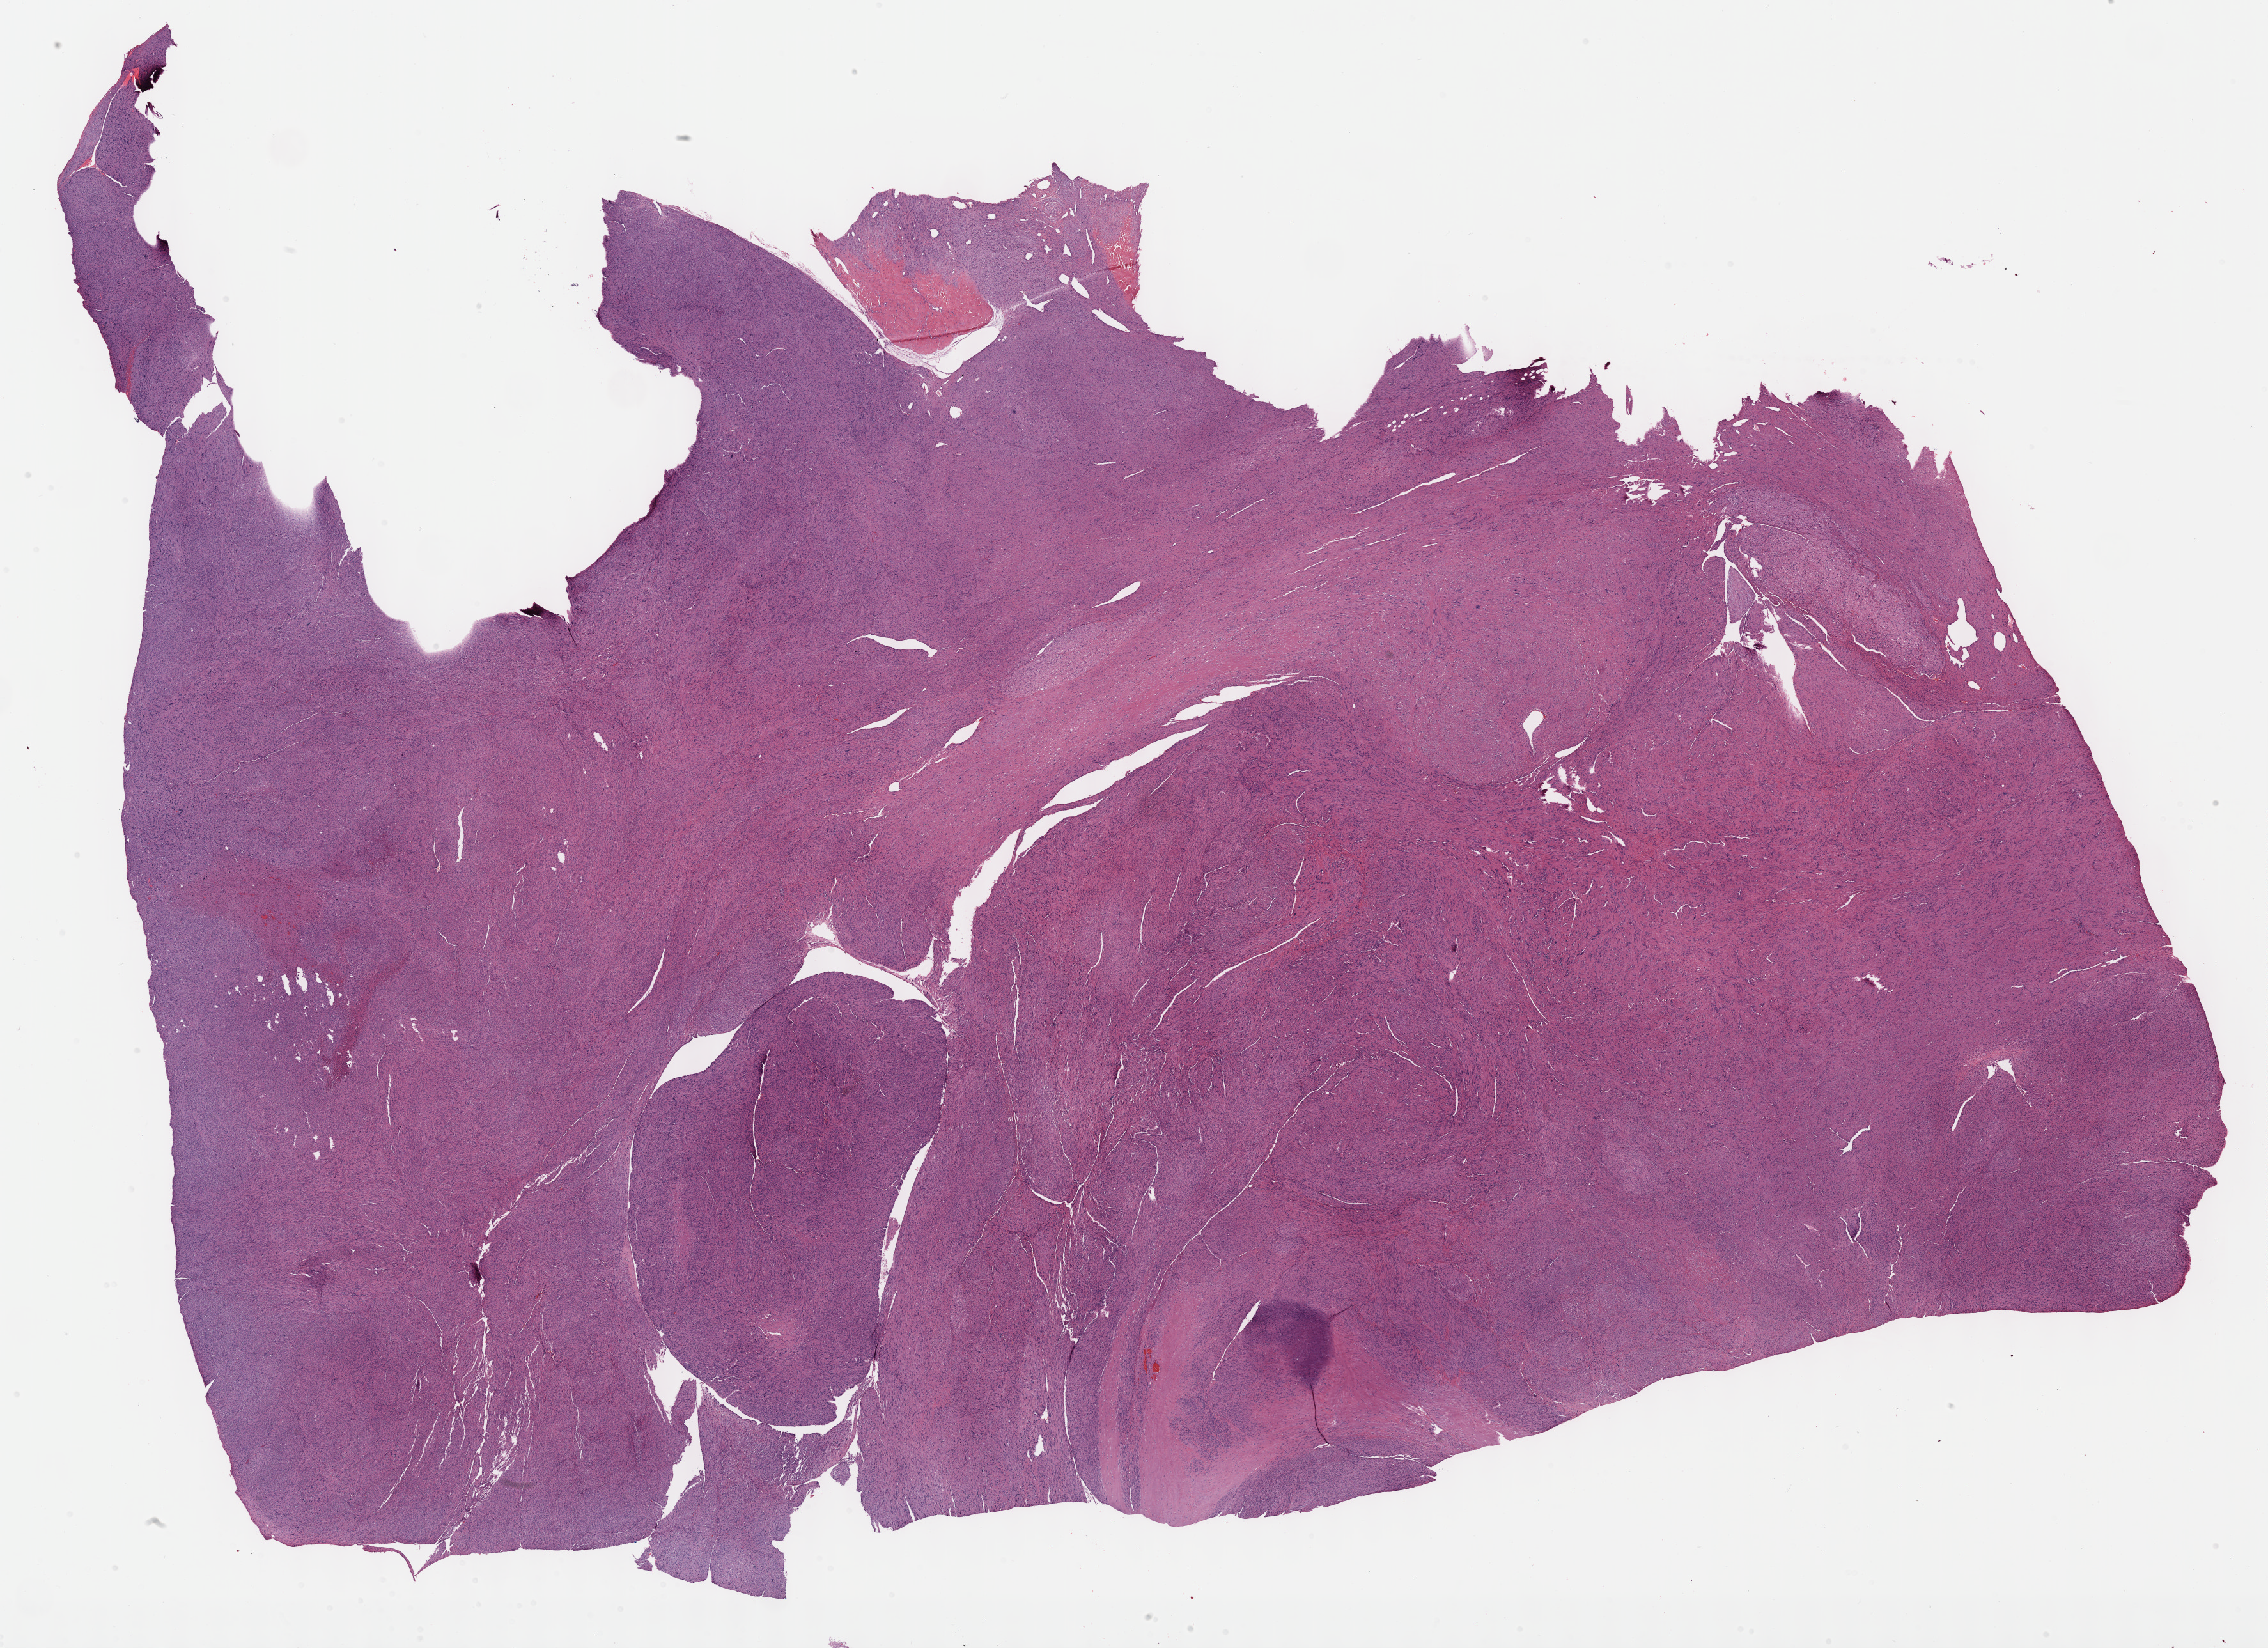
H&E-stained whole-slide image — low-resolution overview of the scanned area, about 28.7 x 20.8 mm, FFPE section, primary tumour sample from the connective, subcutaneous and other soft tissues. Female patient; age at initial diagnosis 66 years.
Pathologic diagnosis: Leiomyosarcoma, NOS (connective, subcutaneous and other soft tissues of trunk, NOS).